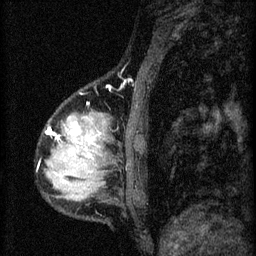
Breast MRI (dynamic contrast-enhanced), one sagittal slice. Position 13 of 60 along the scan axis. 3 images stored at this slice position (order not interpretable as contrast timing). 1.5 T. TE 4.2 ms, TR 8.2 ms. 2 mm slice thickness. 256 × 256 image matrix, field of view 180 × 180 mm. Patient: female, 37 years.
Structures marked on this image (semi-automatically segmented with operator editing):
- analysis volume of interest (the breast-tissue region the enhancement analysis was run in; not a lesion): bounding box (x1, y1, x2, y2) in pixels: (46, 112, 119, 197)
- tumour enhancement mask (voxels above the 70 % enhancement threshold inside the analysis volume of interest): (52, 124, 95, 149)